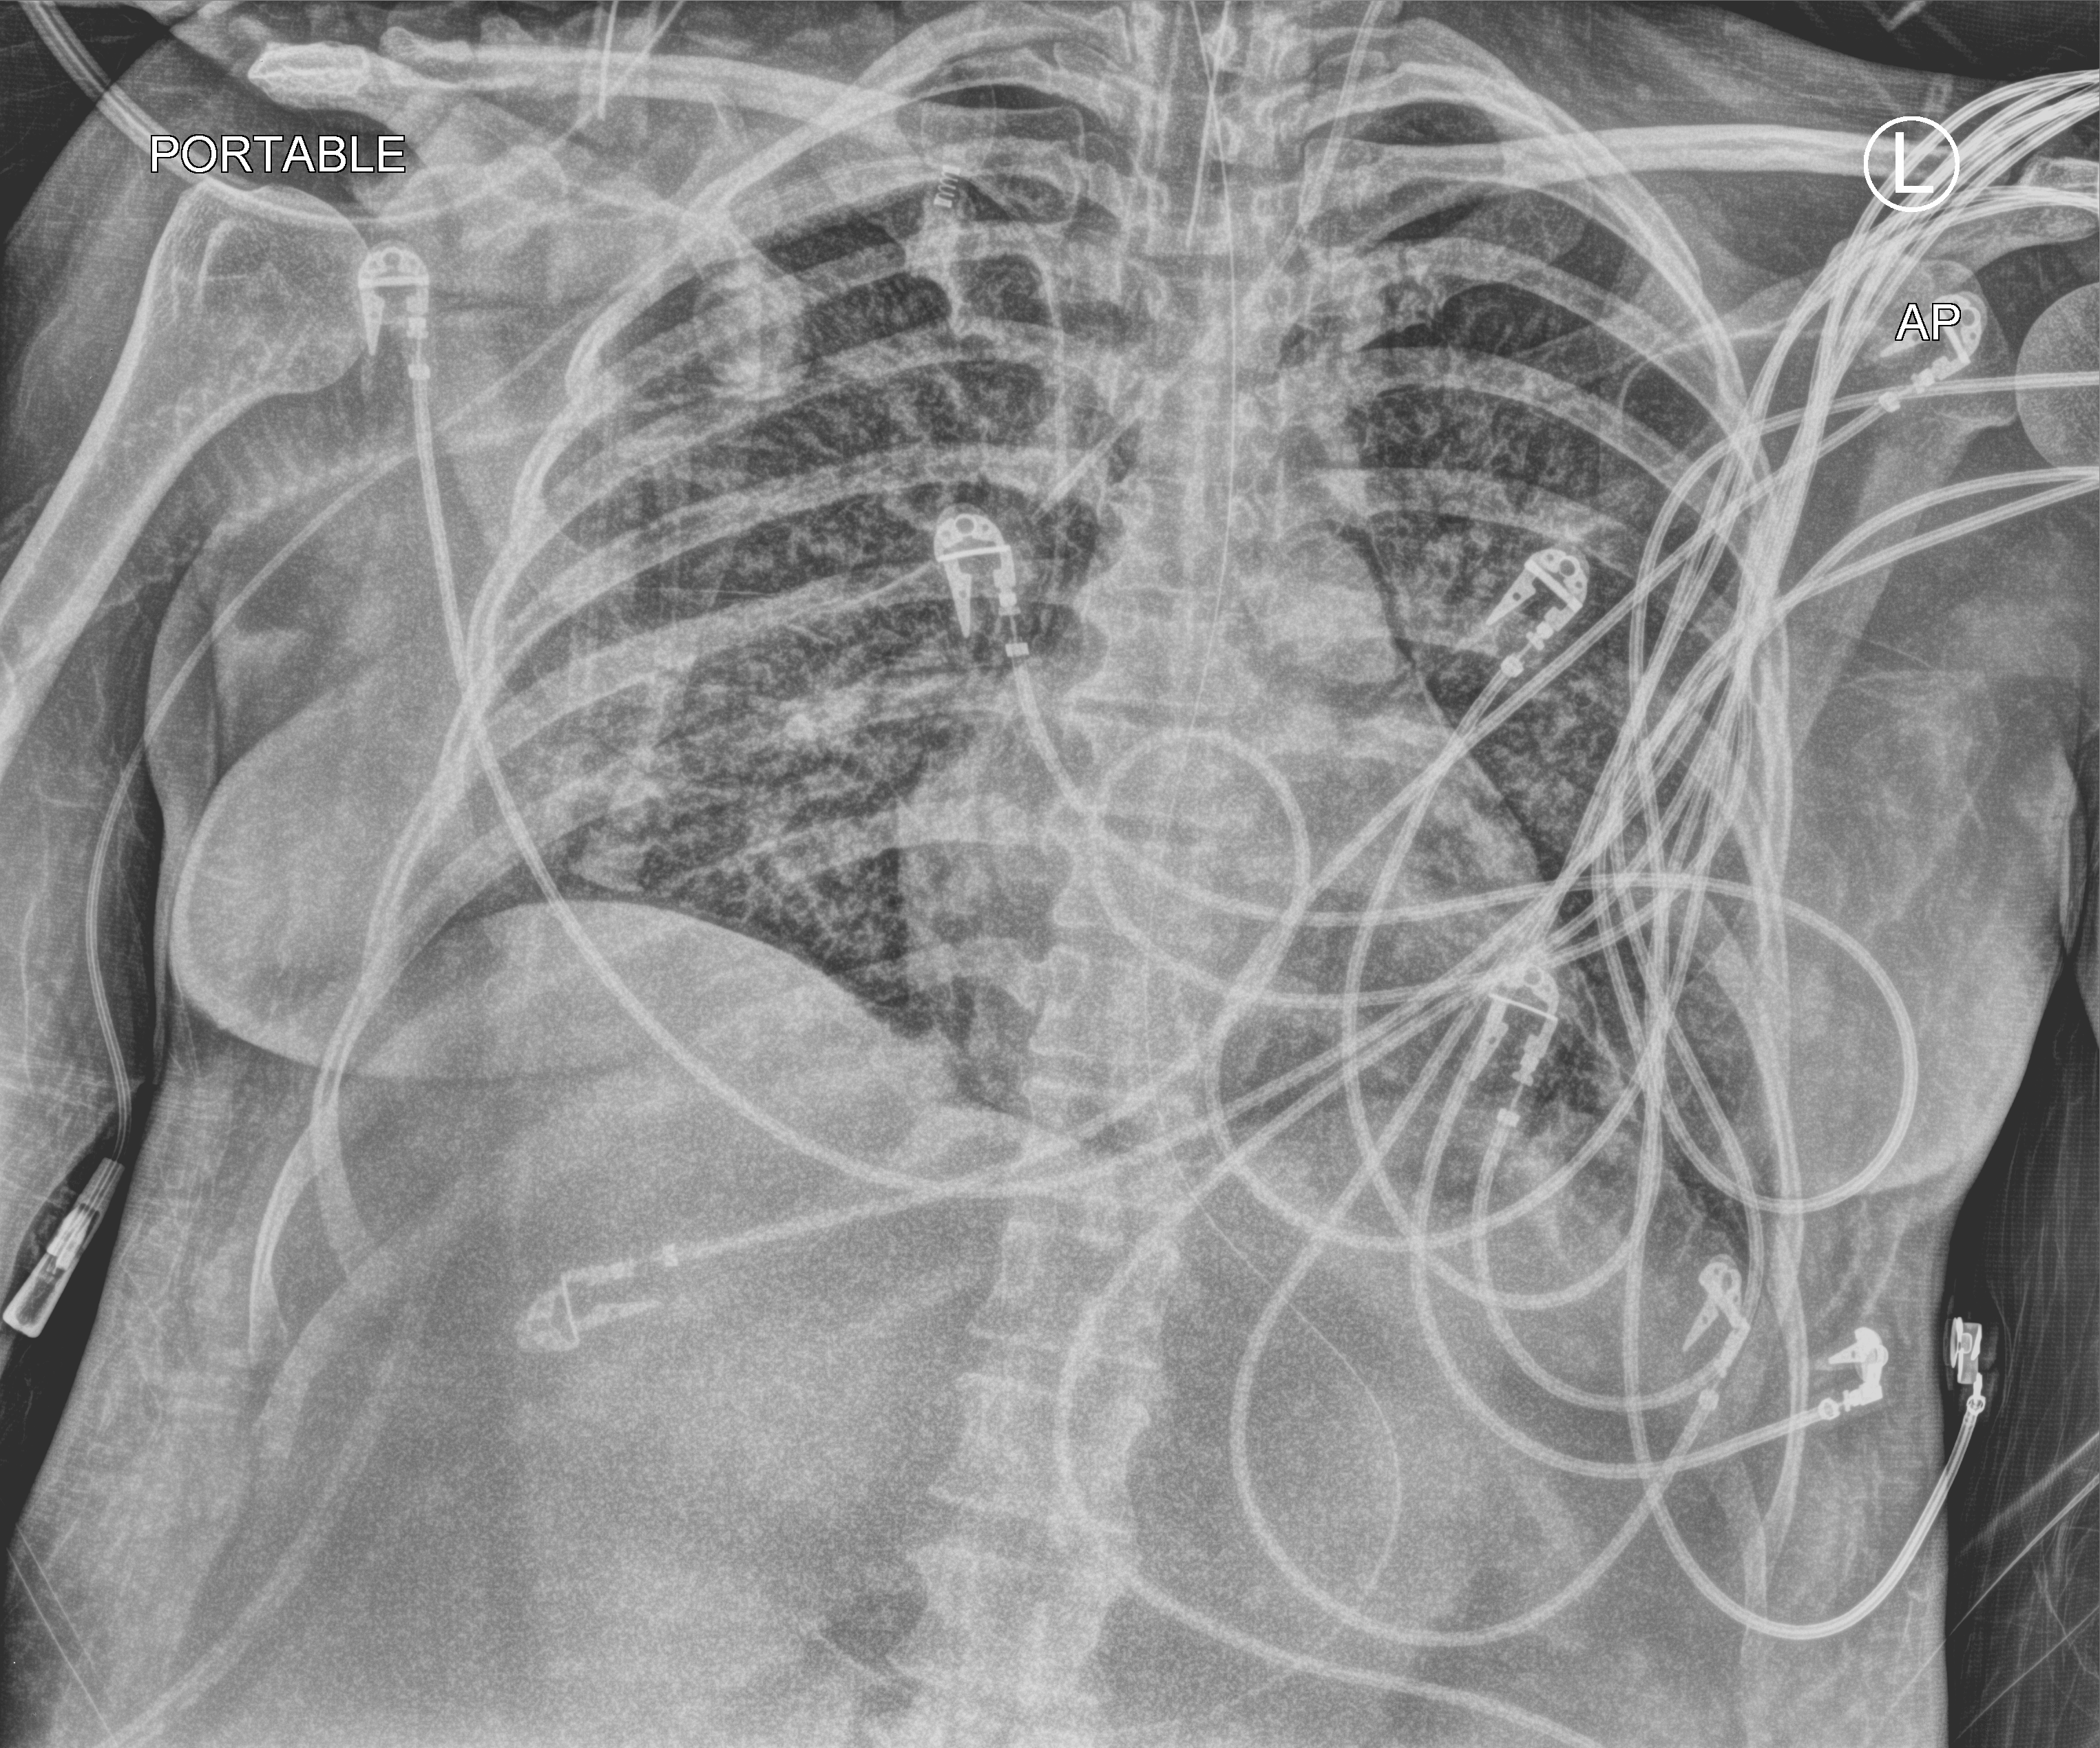
Bedside chest radiograph (computed radiography), anteroposterior (AP) projection. Female patient hospitalised with COVID-19, age 18–59 years.
Hospital-stay facts (about this admission, not read from this image; timing relative to this image not recorded):
- smoking status (admission record): former